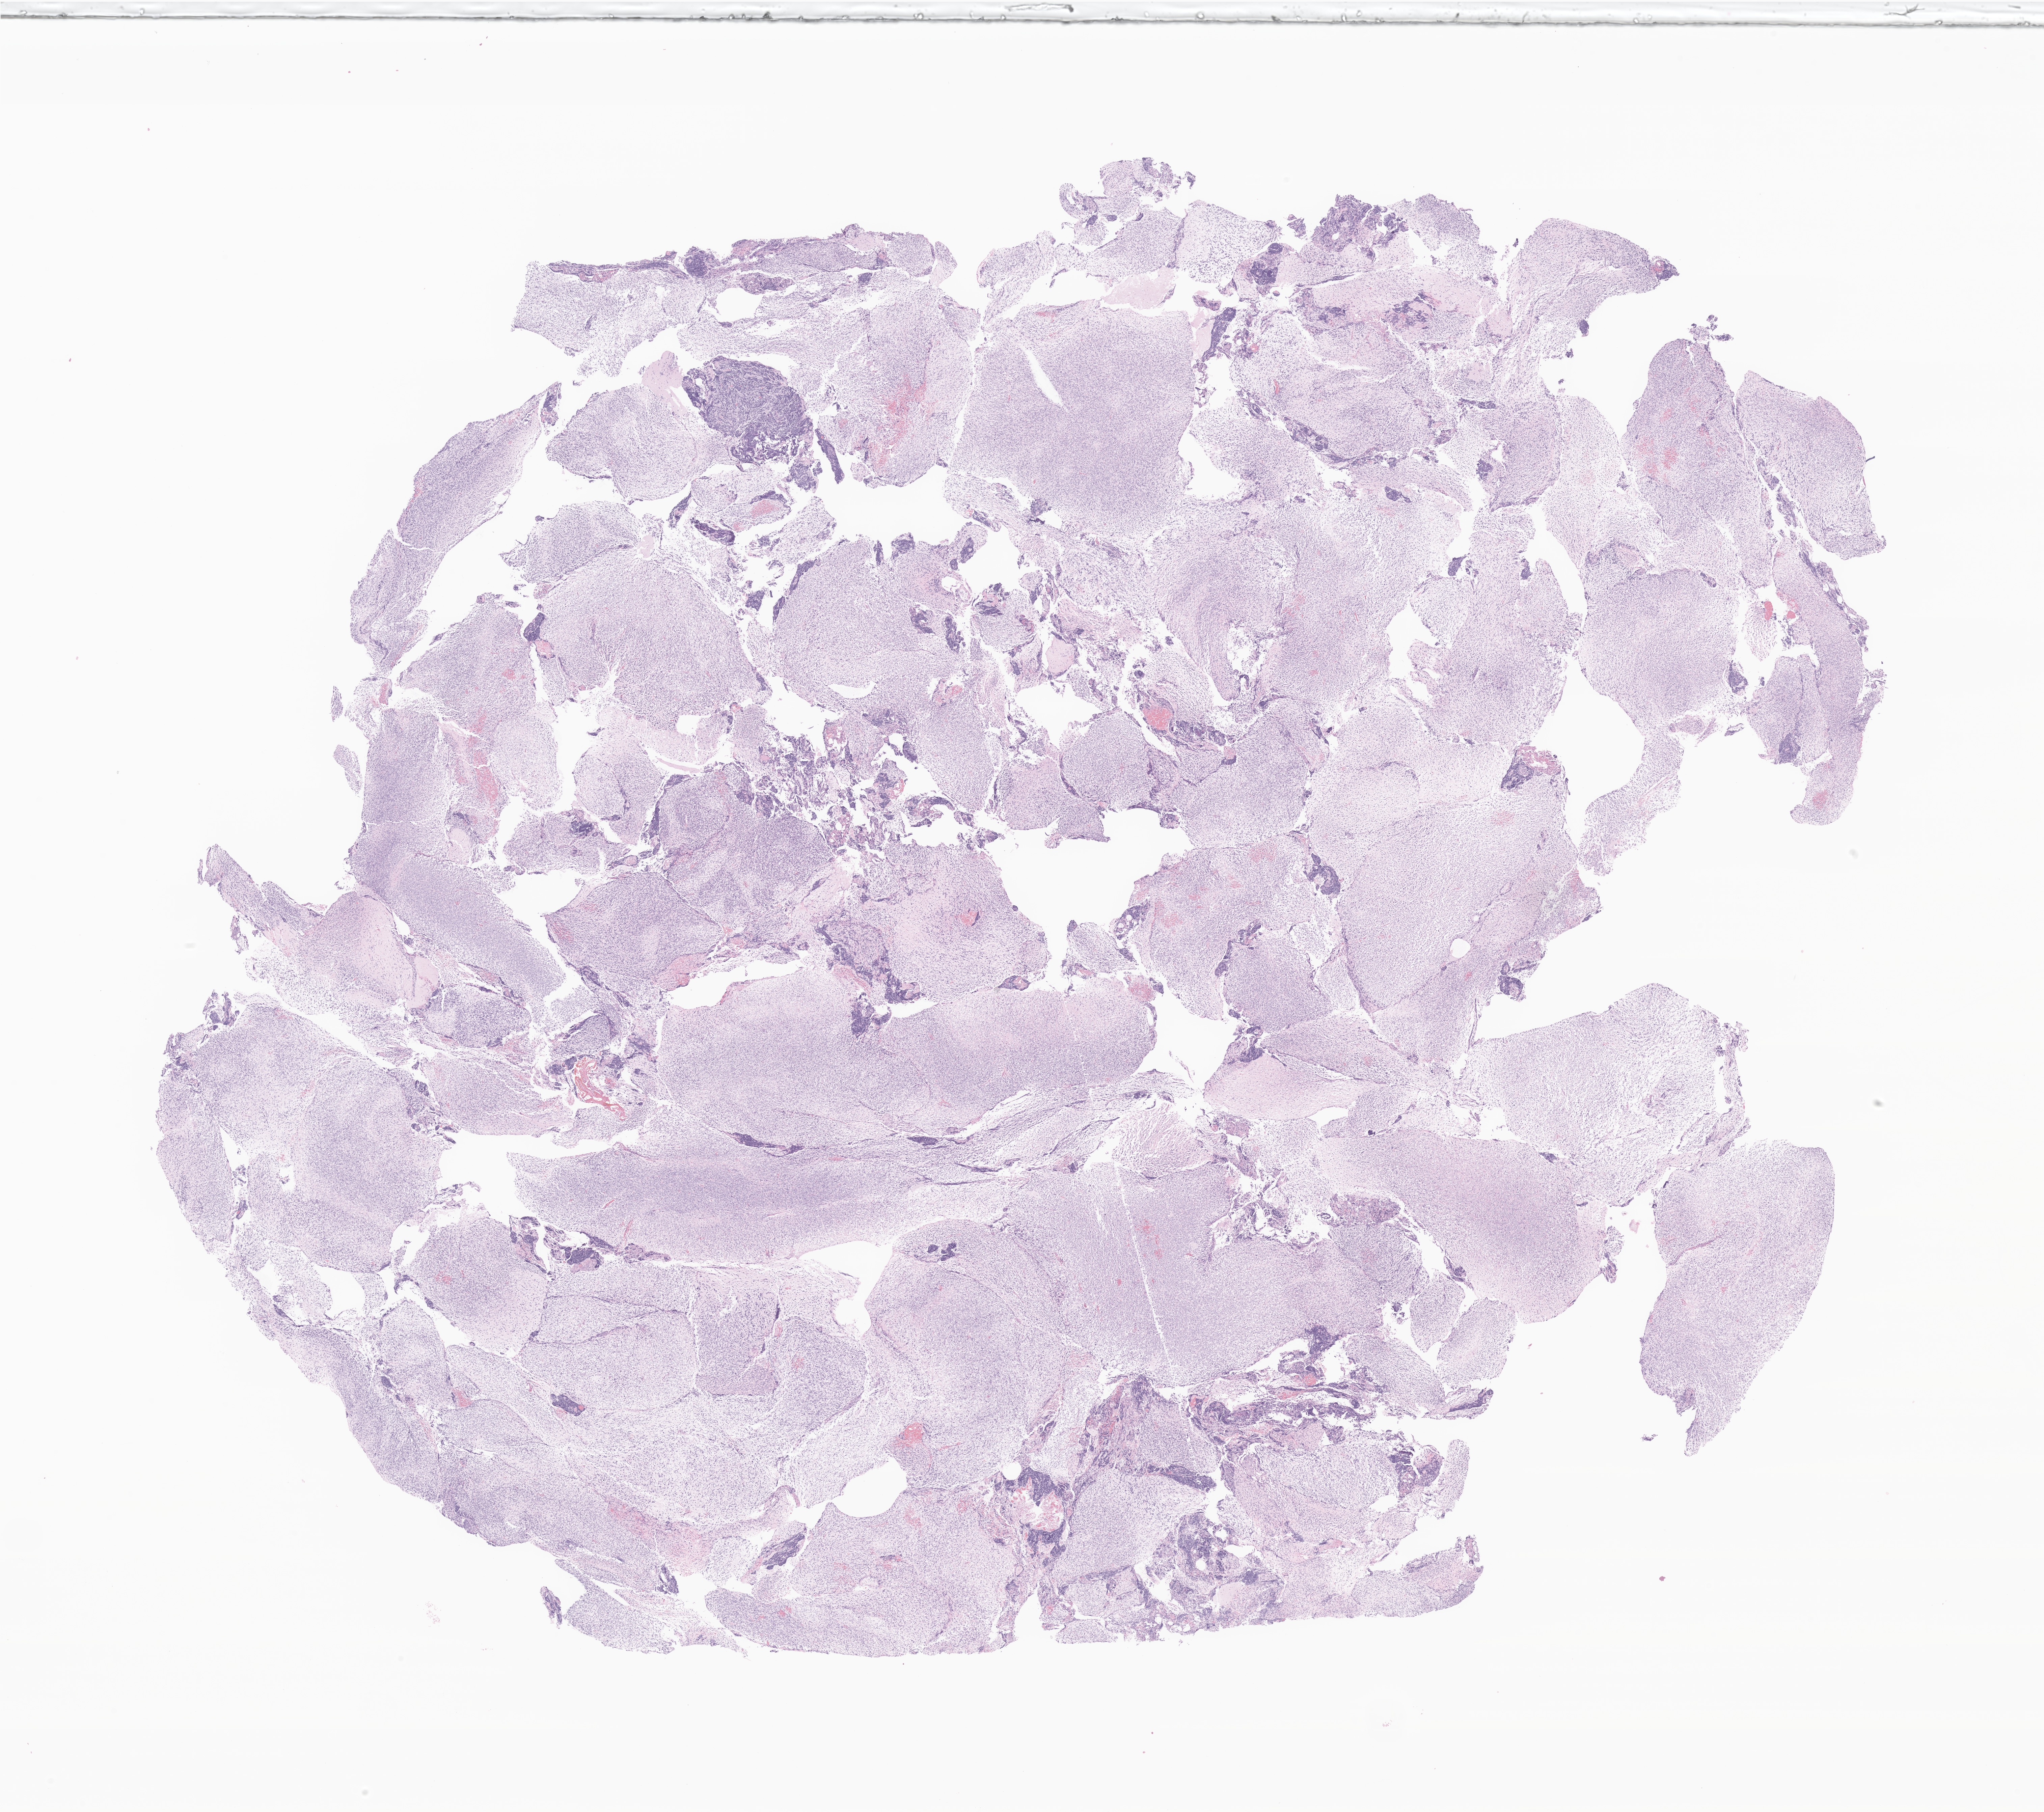
Haematoxylin and eosin whole-slide image of tumor tissue from the brain, a low-resolution overview of the entire scanned area, about 25.5 x 22.6 mm, FFPE section. Patient male; age 145 months.
Recorded diagnosis: Medulloblastoma, NOS.